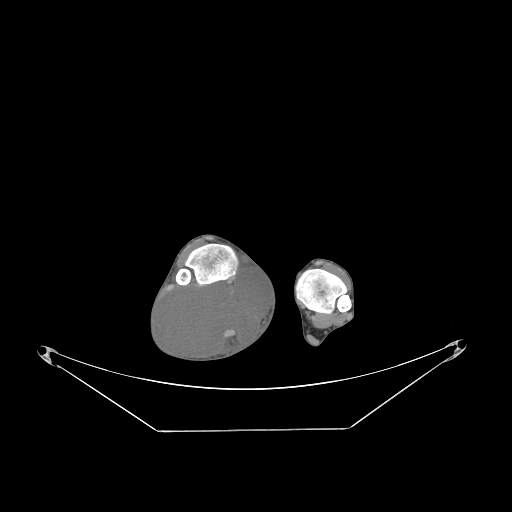
CT of an extremity soft-tissue mass (from a PET/CT study), one axial slice. Position 52 of 267 along the scan axis. Soft-tissue window (W 400 / L 40 HU). 3.75 mm slice thickness. 512 × 512 image matrix, field of view 500 × 500 mm. Male patient. From the clinical record (not read from this slice): histological type: liposarcoma - round cell; grade: high; site of the primary tumour: right calf.
Structures marked on this image (expert contour drawn on MRI and transferred to this co-registered scan by the dataset authors):
- gross tumour volume (mass): bounding box <162,272,268,359> (left, top, right, bottom; pixels)